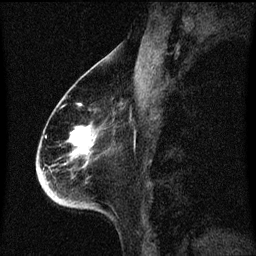
Breast MRI (dynamic contrast-enhanced), one sagittal slice. Position 30 of 60 along the scan axis. Dynamic contrast-enhanced series, image 2 of 3 at this slice position (ordered by acquisition). 1.5 T. TE 4.2 ms, TR 8.4 ms. 2 mm slice thickness. 256 × 256 image matrix. Female patient, age 68 years. From the clinical record (not read from this slice): setting: breast cancer imaged before/during neoadjuvant chemotherapy; receptor status: triple-negative.
Structures marked on this image (semi-automatically segmented with operator editing):
- analysis volume of interest (the breast-tissue region the enhancement analysis was run in; not a lesion): bounding box [x1, y1, x2, y2] px = [39, 96, 111, 213]
- tumour enhancement mask (voxels above the 70 % enhancement threshold inside the analysis volume of interest): [70, 104, 94, 157]